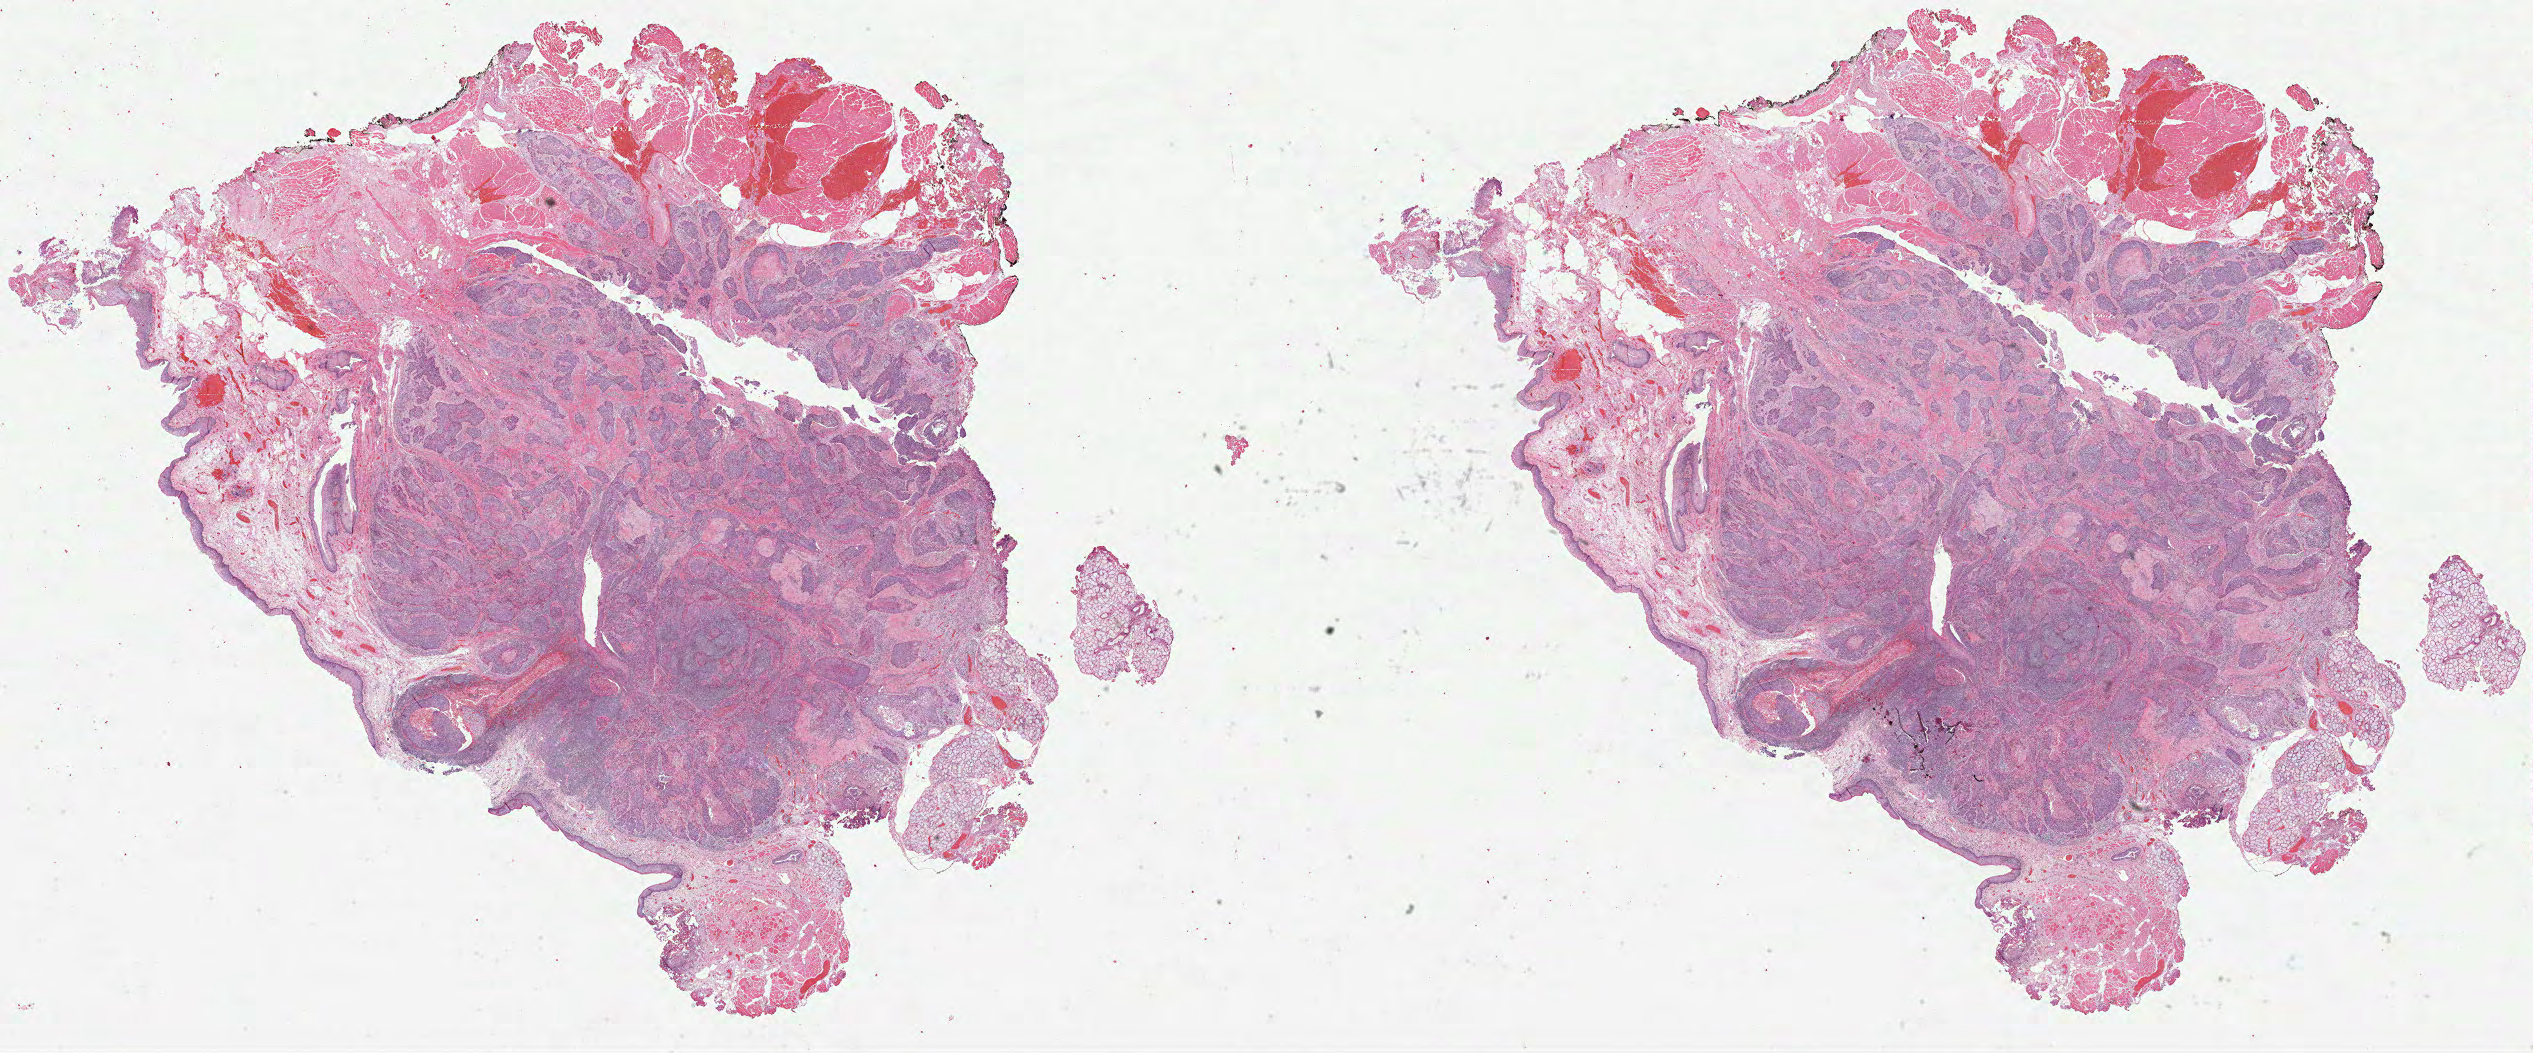
H&E whole-slide image — a low-resolution overview of the entire scanned area, about 40.9 x 17.0 mm, FFPE section, sample: primary tumour, head and neck. Patient: female, age at initial diagnosis 56 years.
Pathologic diagnosis: Squamous cell carcinoma, NOS (tonsil, NOS).